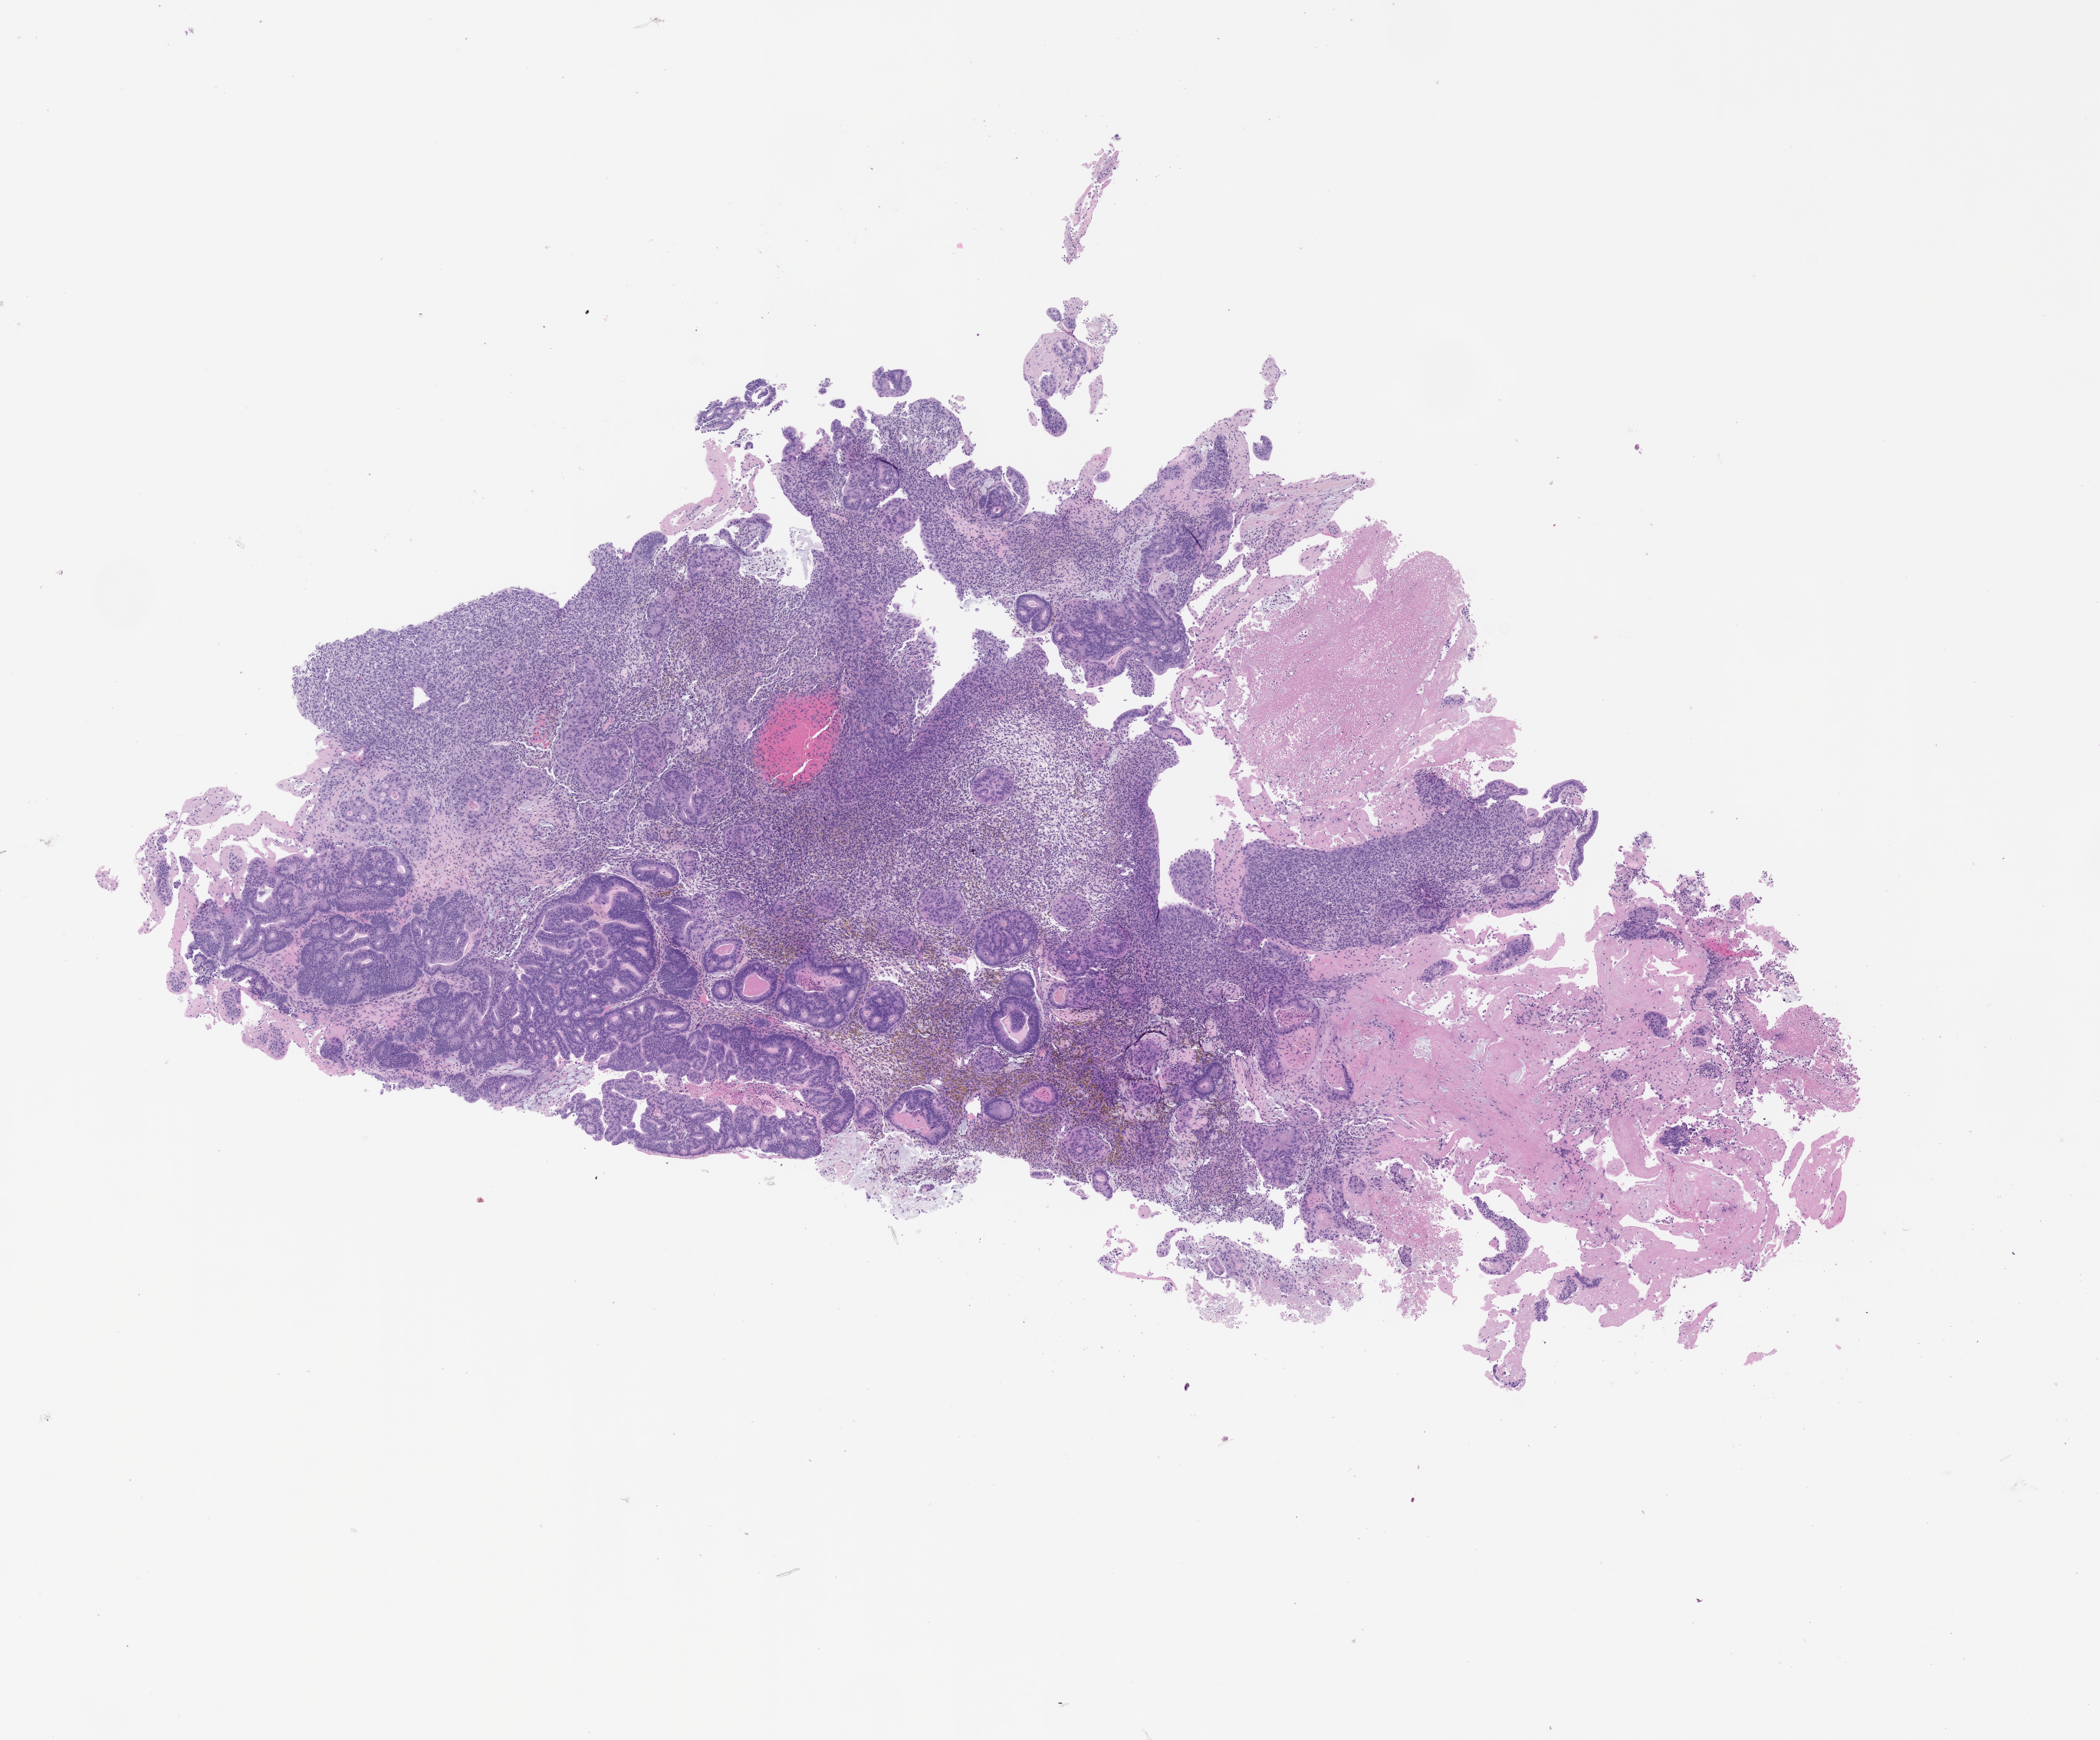
Whole-slide image, haematoxylin and eosin: patient-derived xenograft (human tumor grown in a mouse), passage 4, low-resolution overview of the scanned area, about 11.0 x 9.1 mm. FFPE section. Tumor site category: colon.
Originating patient diagnosis: Colon Adenocarcinoma.